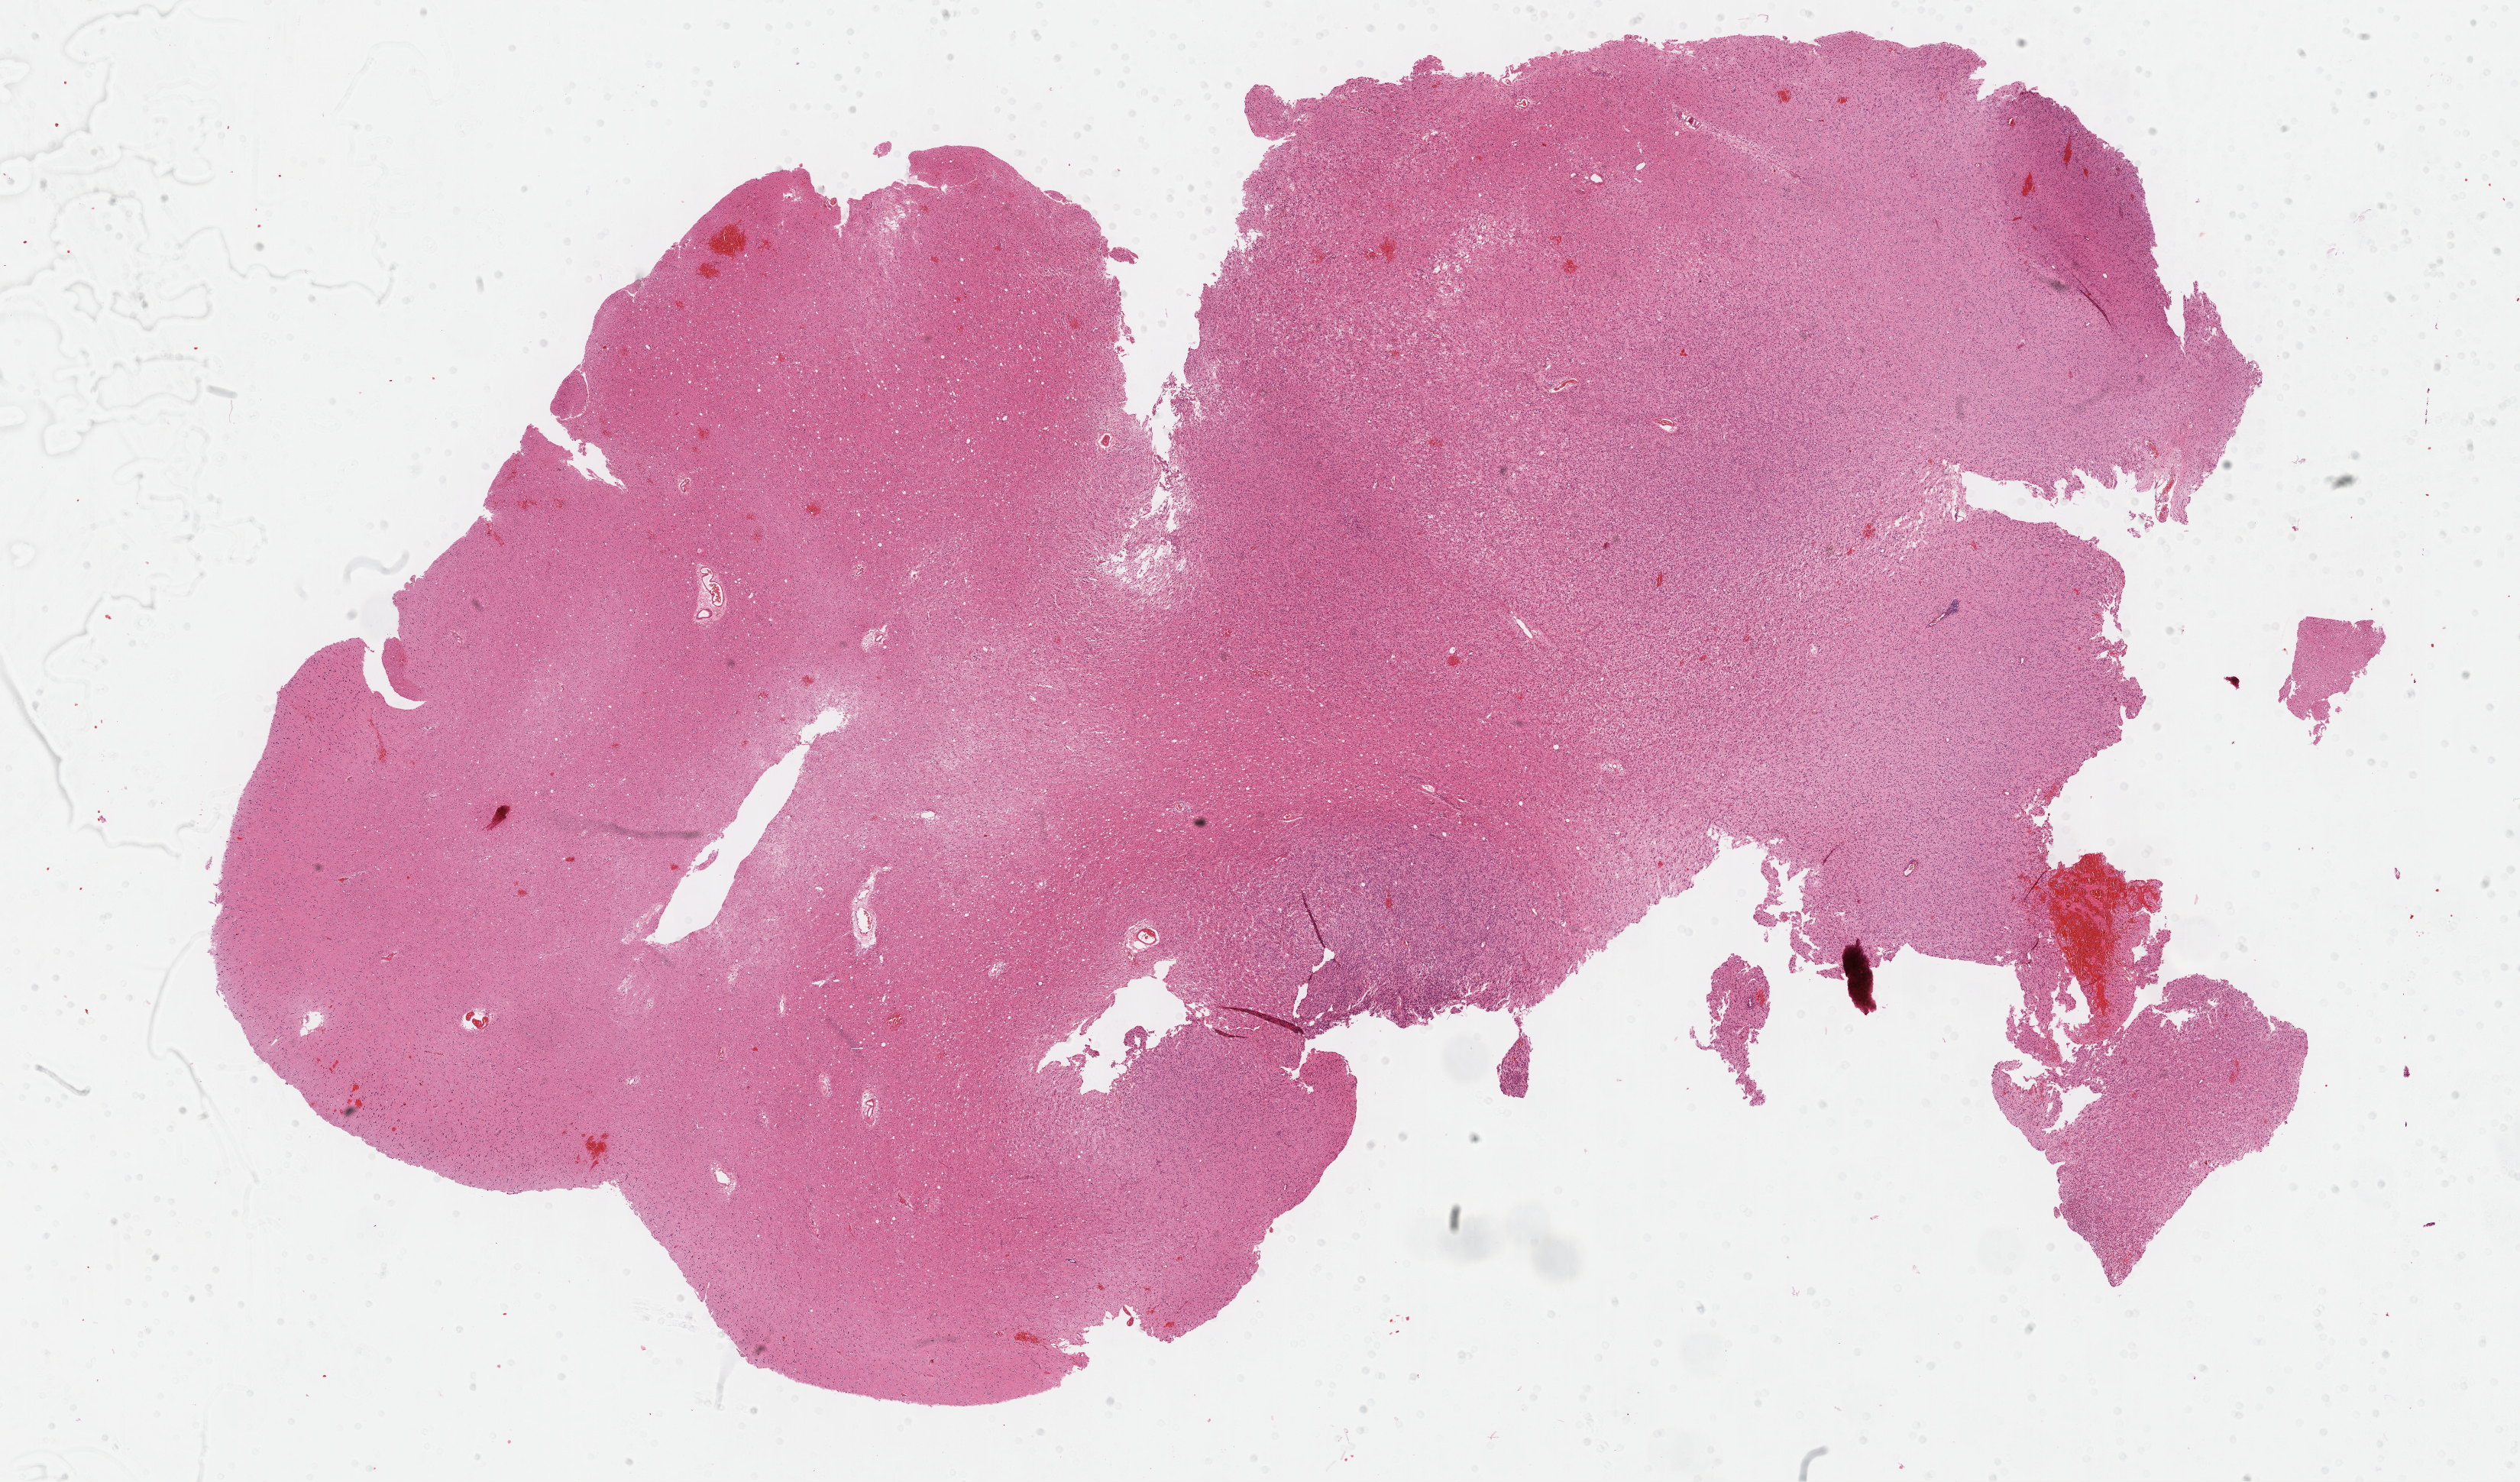
H&E-stained whole-slide image — shown as a low-resolution overview of the whole scanned area (about 26.7 x 15.7 mm); formalin-fixed paraffin-embedded (FFPE) diagnostic section; primary tumour sample from the brain. Female patient; age at initial diagnosis 59 years. Histologic grade: G3 (poorly differentiated).
Diagnosis: Astrocytoma, anaplastic (cerebrum). Laterality: left.